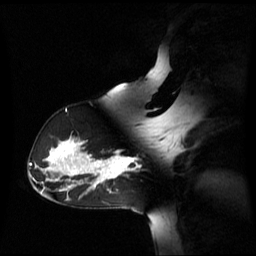
Breast MRI (dynamic contrast-enhanced), one sagittal slice. Slice 41 of 60 in the series (ordered by position). Dynamic contrast-enhanced series, image 2 of 3 at this slice position (ordered by acquisition). 1.5 T. TE 4.2 ms, TR 8.4 ms. 2.6 mm slice thickness. 256 × 256 image matrix, field of view 270 × 270 mm. Patient: female, 39 years. Case-level facts recorded for this patient, not image findings: setting: breast cancer imaged before/during neoadjuvant chemotherapy; receptor status: triple-negative.
Annotated regions visible in this slice (semi-automatically segmented with operator editing):
- analysis volume of interest (the breast-tissue region the enhancement analysis was run in; not a lesion): box from (x=105, y=156) to (x=139, y=179) px
- tumour enhancement mask (voxels above the 70 % enhancement threshold inside the analysis volume of interest): (x=105, y=156)–(x=136, y=179)